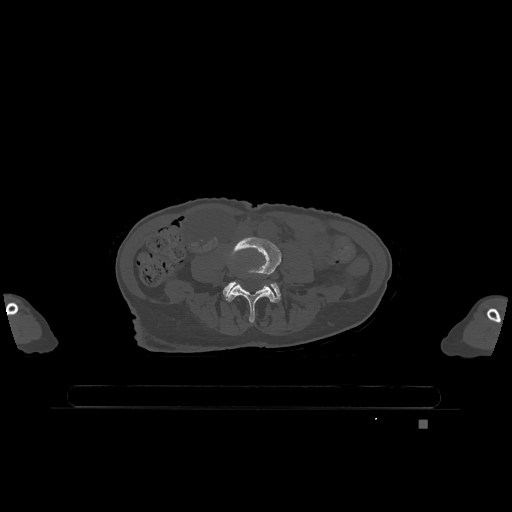
CT including the spine, one axial slice. Position 283 of 1317 along the scan axis. Bone window (W 1800 / L 400 HU). 0.5 mm slice thickness. 512 × 512 image matrix, field of view 500 × 500 mm. Patient: female, 74 years. From the clinical record (not read from this slice): primary cancer: lung; vertebrae with lytic lesions (as recorded): T1, T4, T5, T6, L4, L5.
Annotated regions visible in this slice (semi-automatic segmentation, software-assisted and operator-edited):
- L4 vertebra: bounding box [x1, y1, x2, y2] px = [226, 236, 281, 323]
- L5 vertebra: [223, 281, 281, 302]